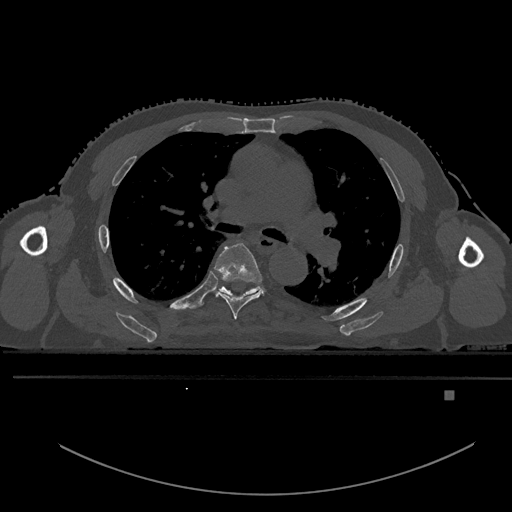
CT including the spine, one axial slice. Slice 343 of 969 in the series (ordered by position). Bone window (W 1800 / L 400 HU). 0.5 mm slice thickness. 512 × 512 image matrix, field of view 456 × 456 mm. Male patient, age 82 years. From the clinical record (not read from this slice): primary cancer: prostate.
Annotated regions visible in this slice (semi-automatic segmentation, software-assisted and operator-edited):
- T5 vertebra: bounding box <214,243,263,320> (left, top, right, bottom; pixels)
- T6 vertebra: <216,286,261,297>